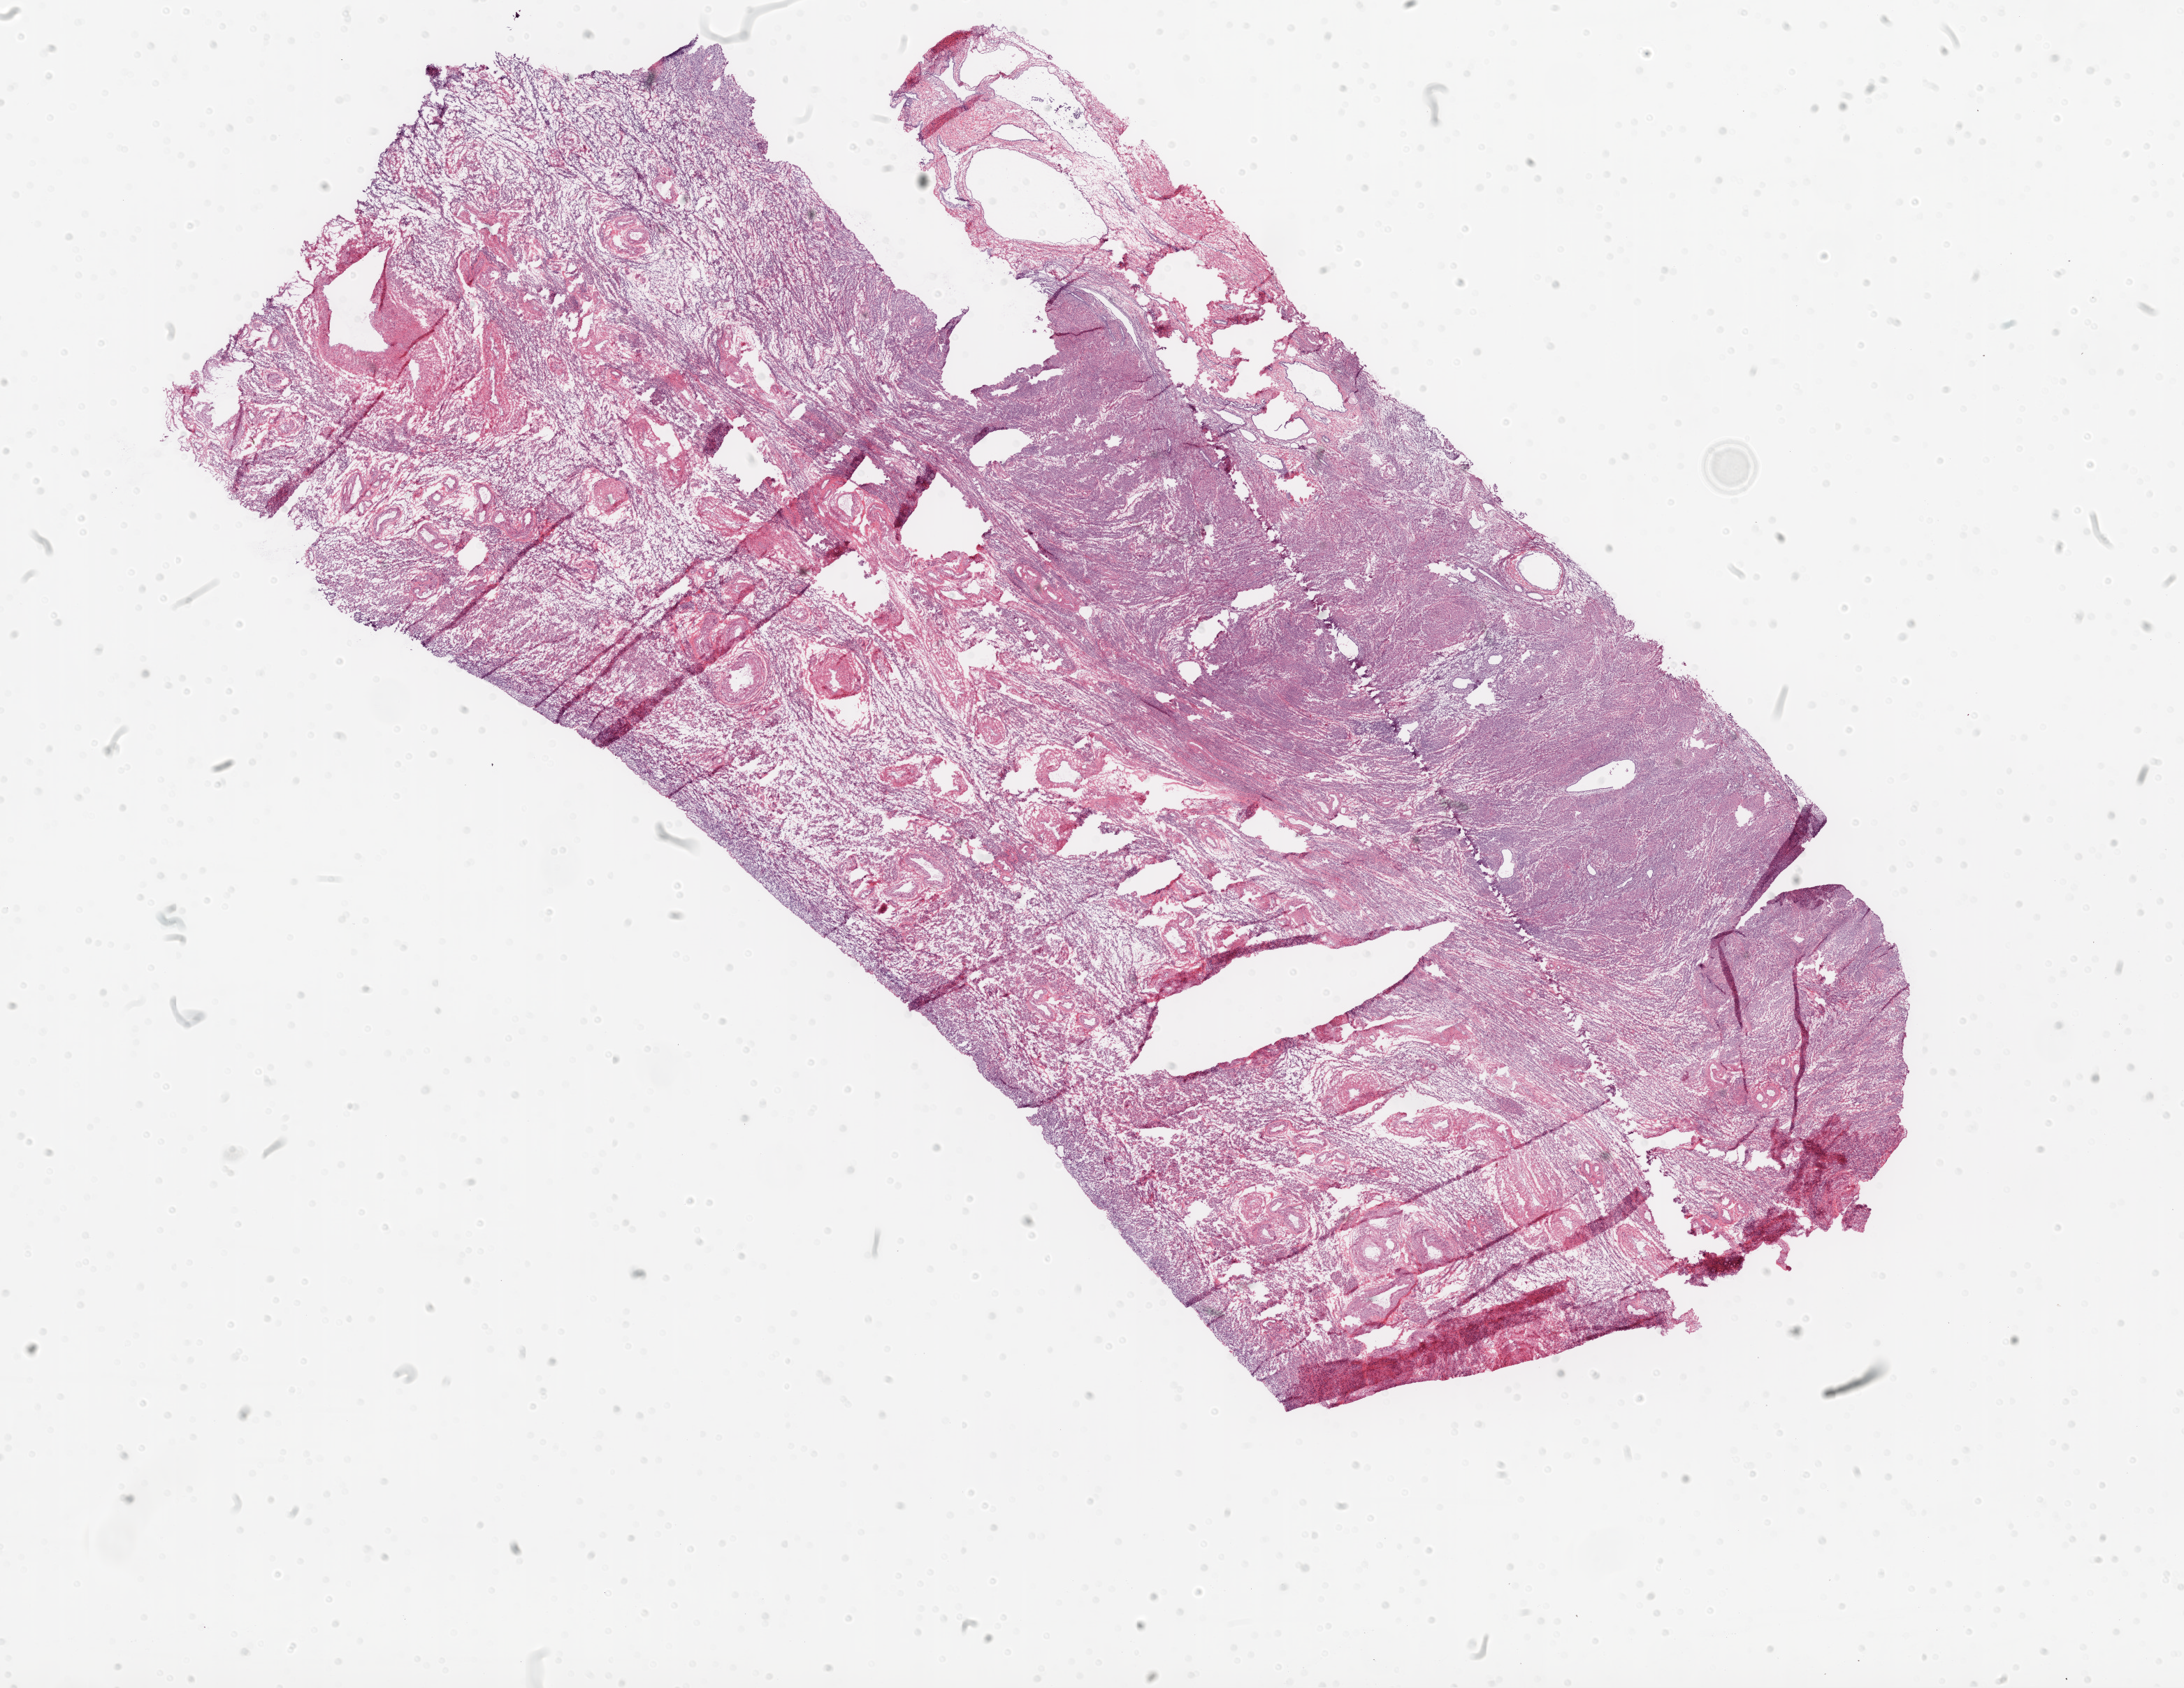
H&E-stained whole-slide image, a low-resolution overview of the entire scanned area, about 25.1 x 19.4 mm. Frozen section from the bottom of the tissue portion. Ovary, solid tissue normal (non-tumour tissue) sample. Female patient; age at initial diagnosis 62 years.
This section: solid tissue normal (non-tumour) sample from the same patient. Patient diagnosis: Serous cystadenocarcinoma, NOS.